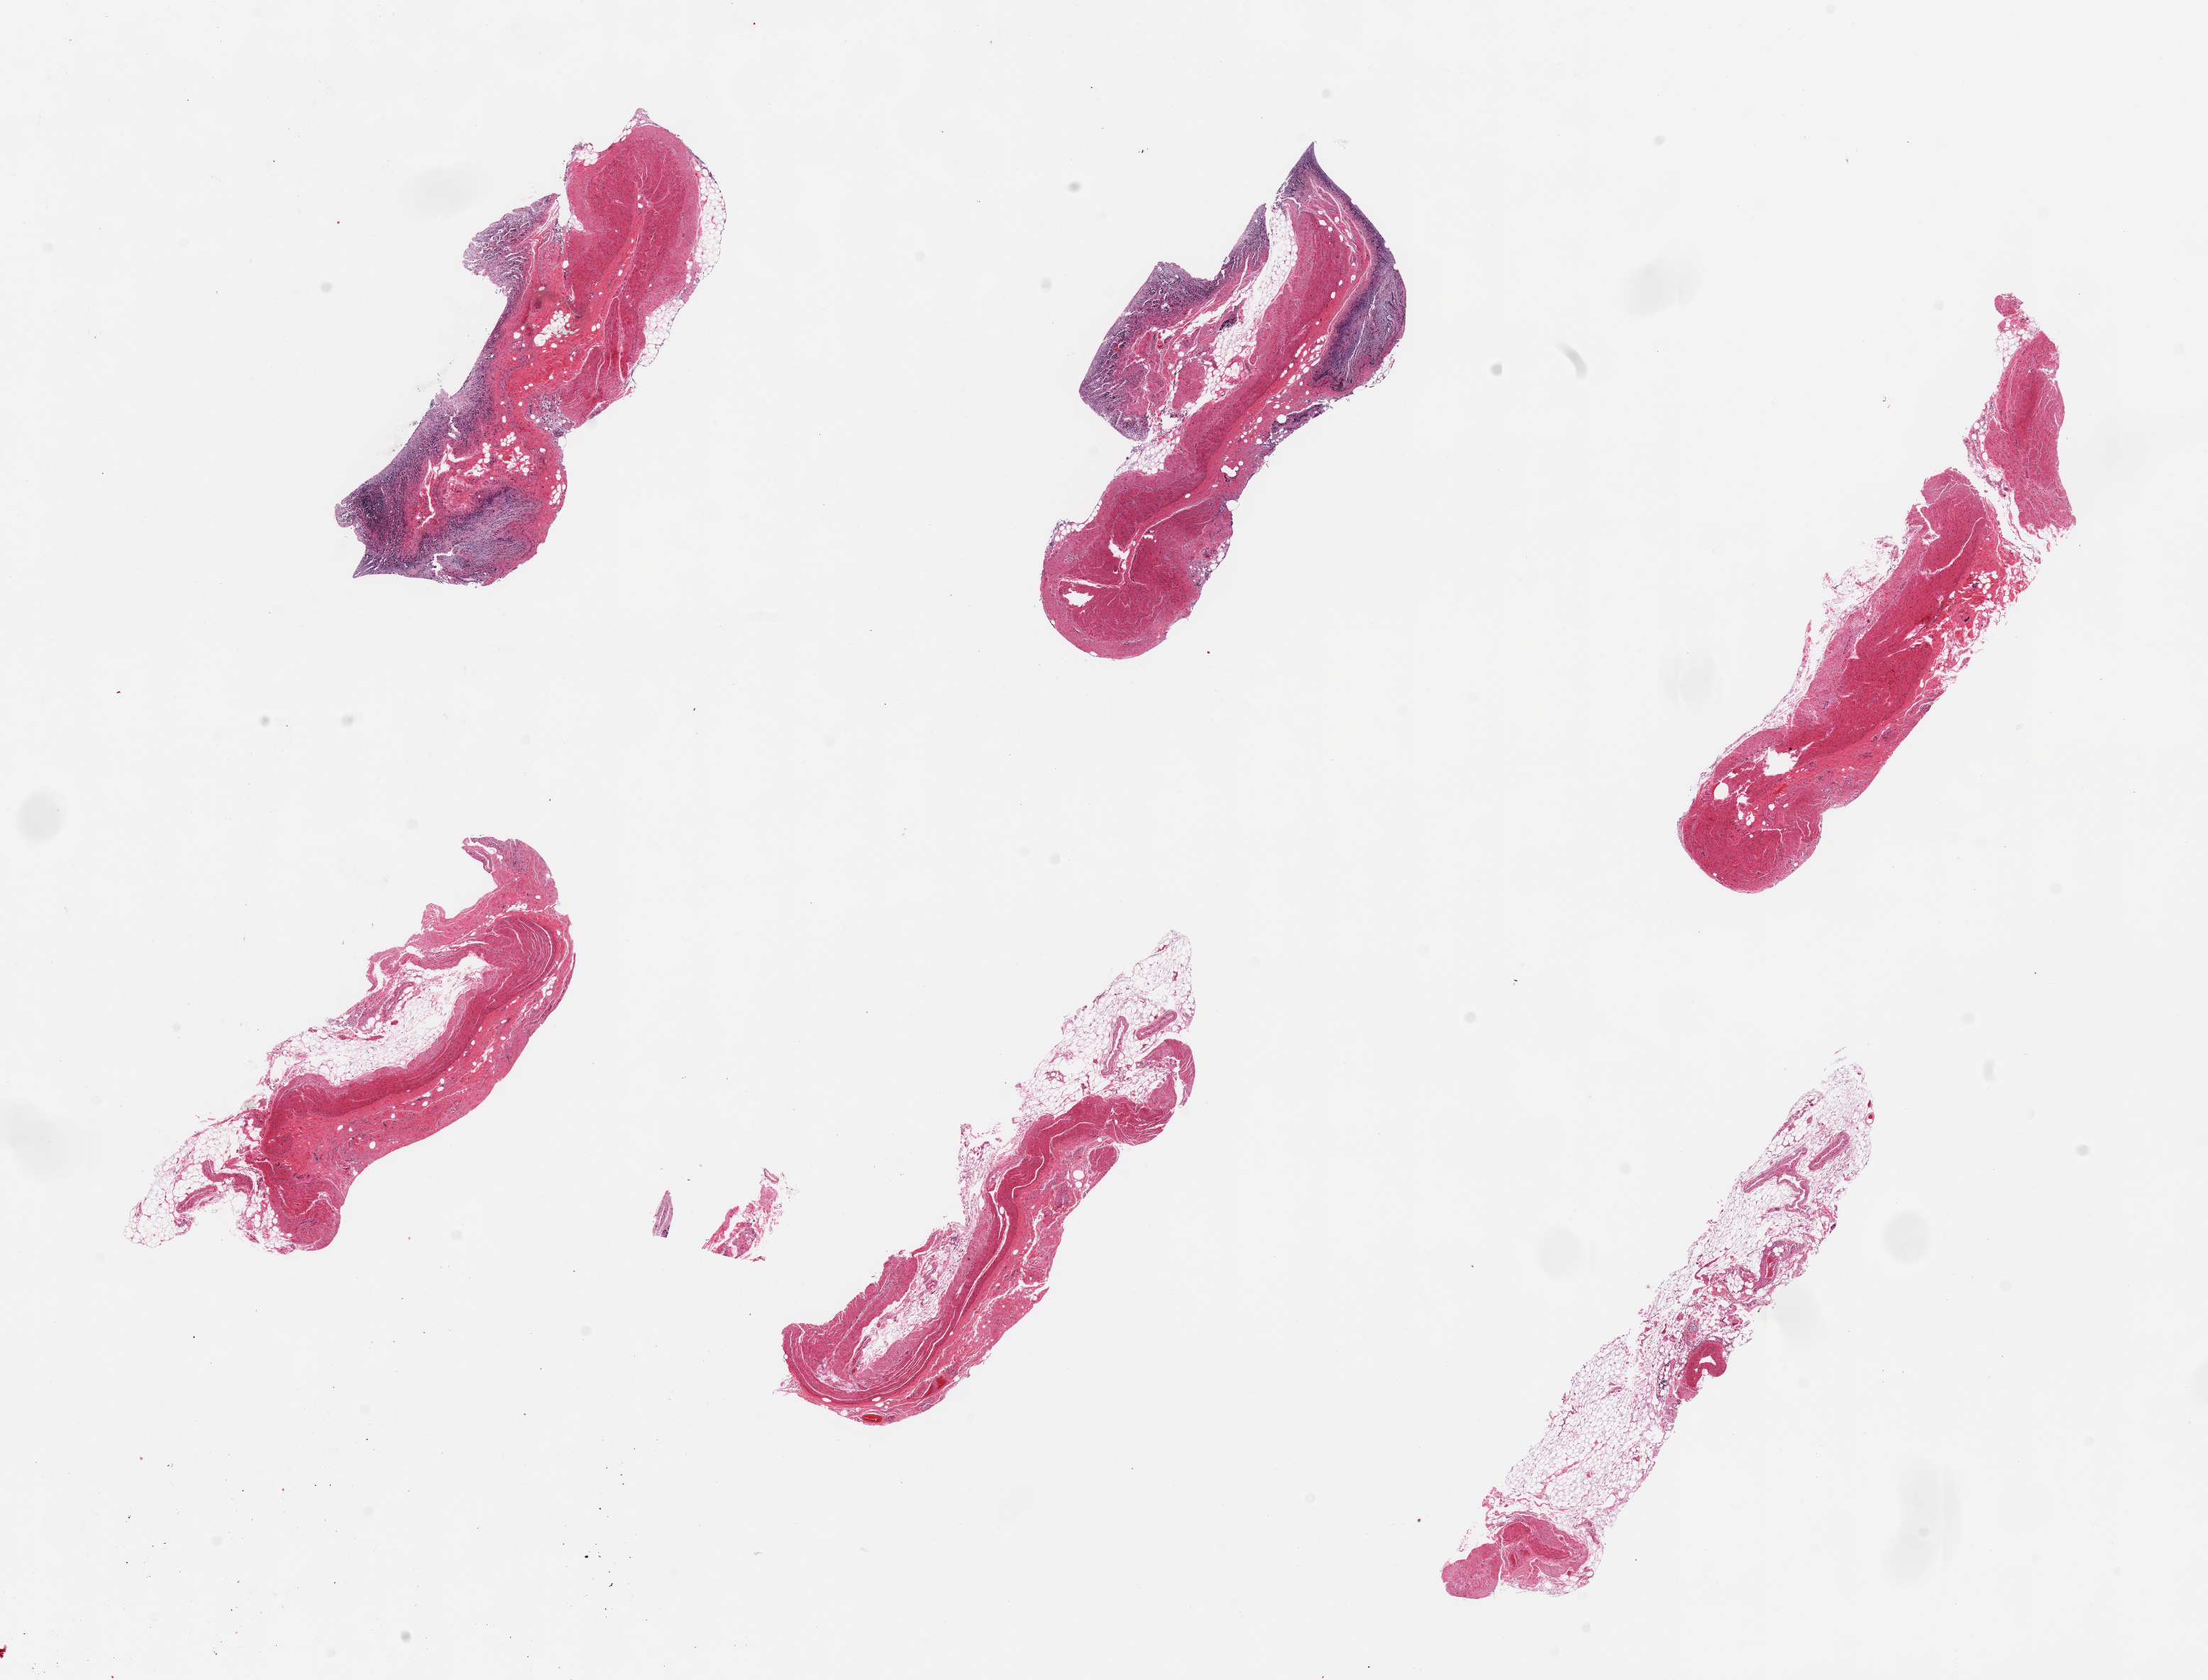
Haematoxylin and eosin whole-slide image — a low-resolution overview of the entire scanned area, about 24.6 x 18.7 mm (from a 20x scan). Donor: male.
Specimen: PAXgene-fixed paraffin-embedded (PFPE) section; target tissue: sigmoid colon; tissue donor sample.